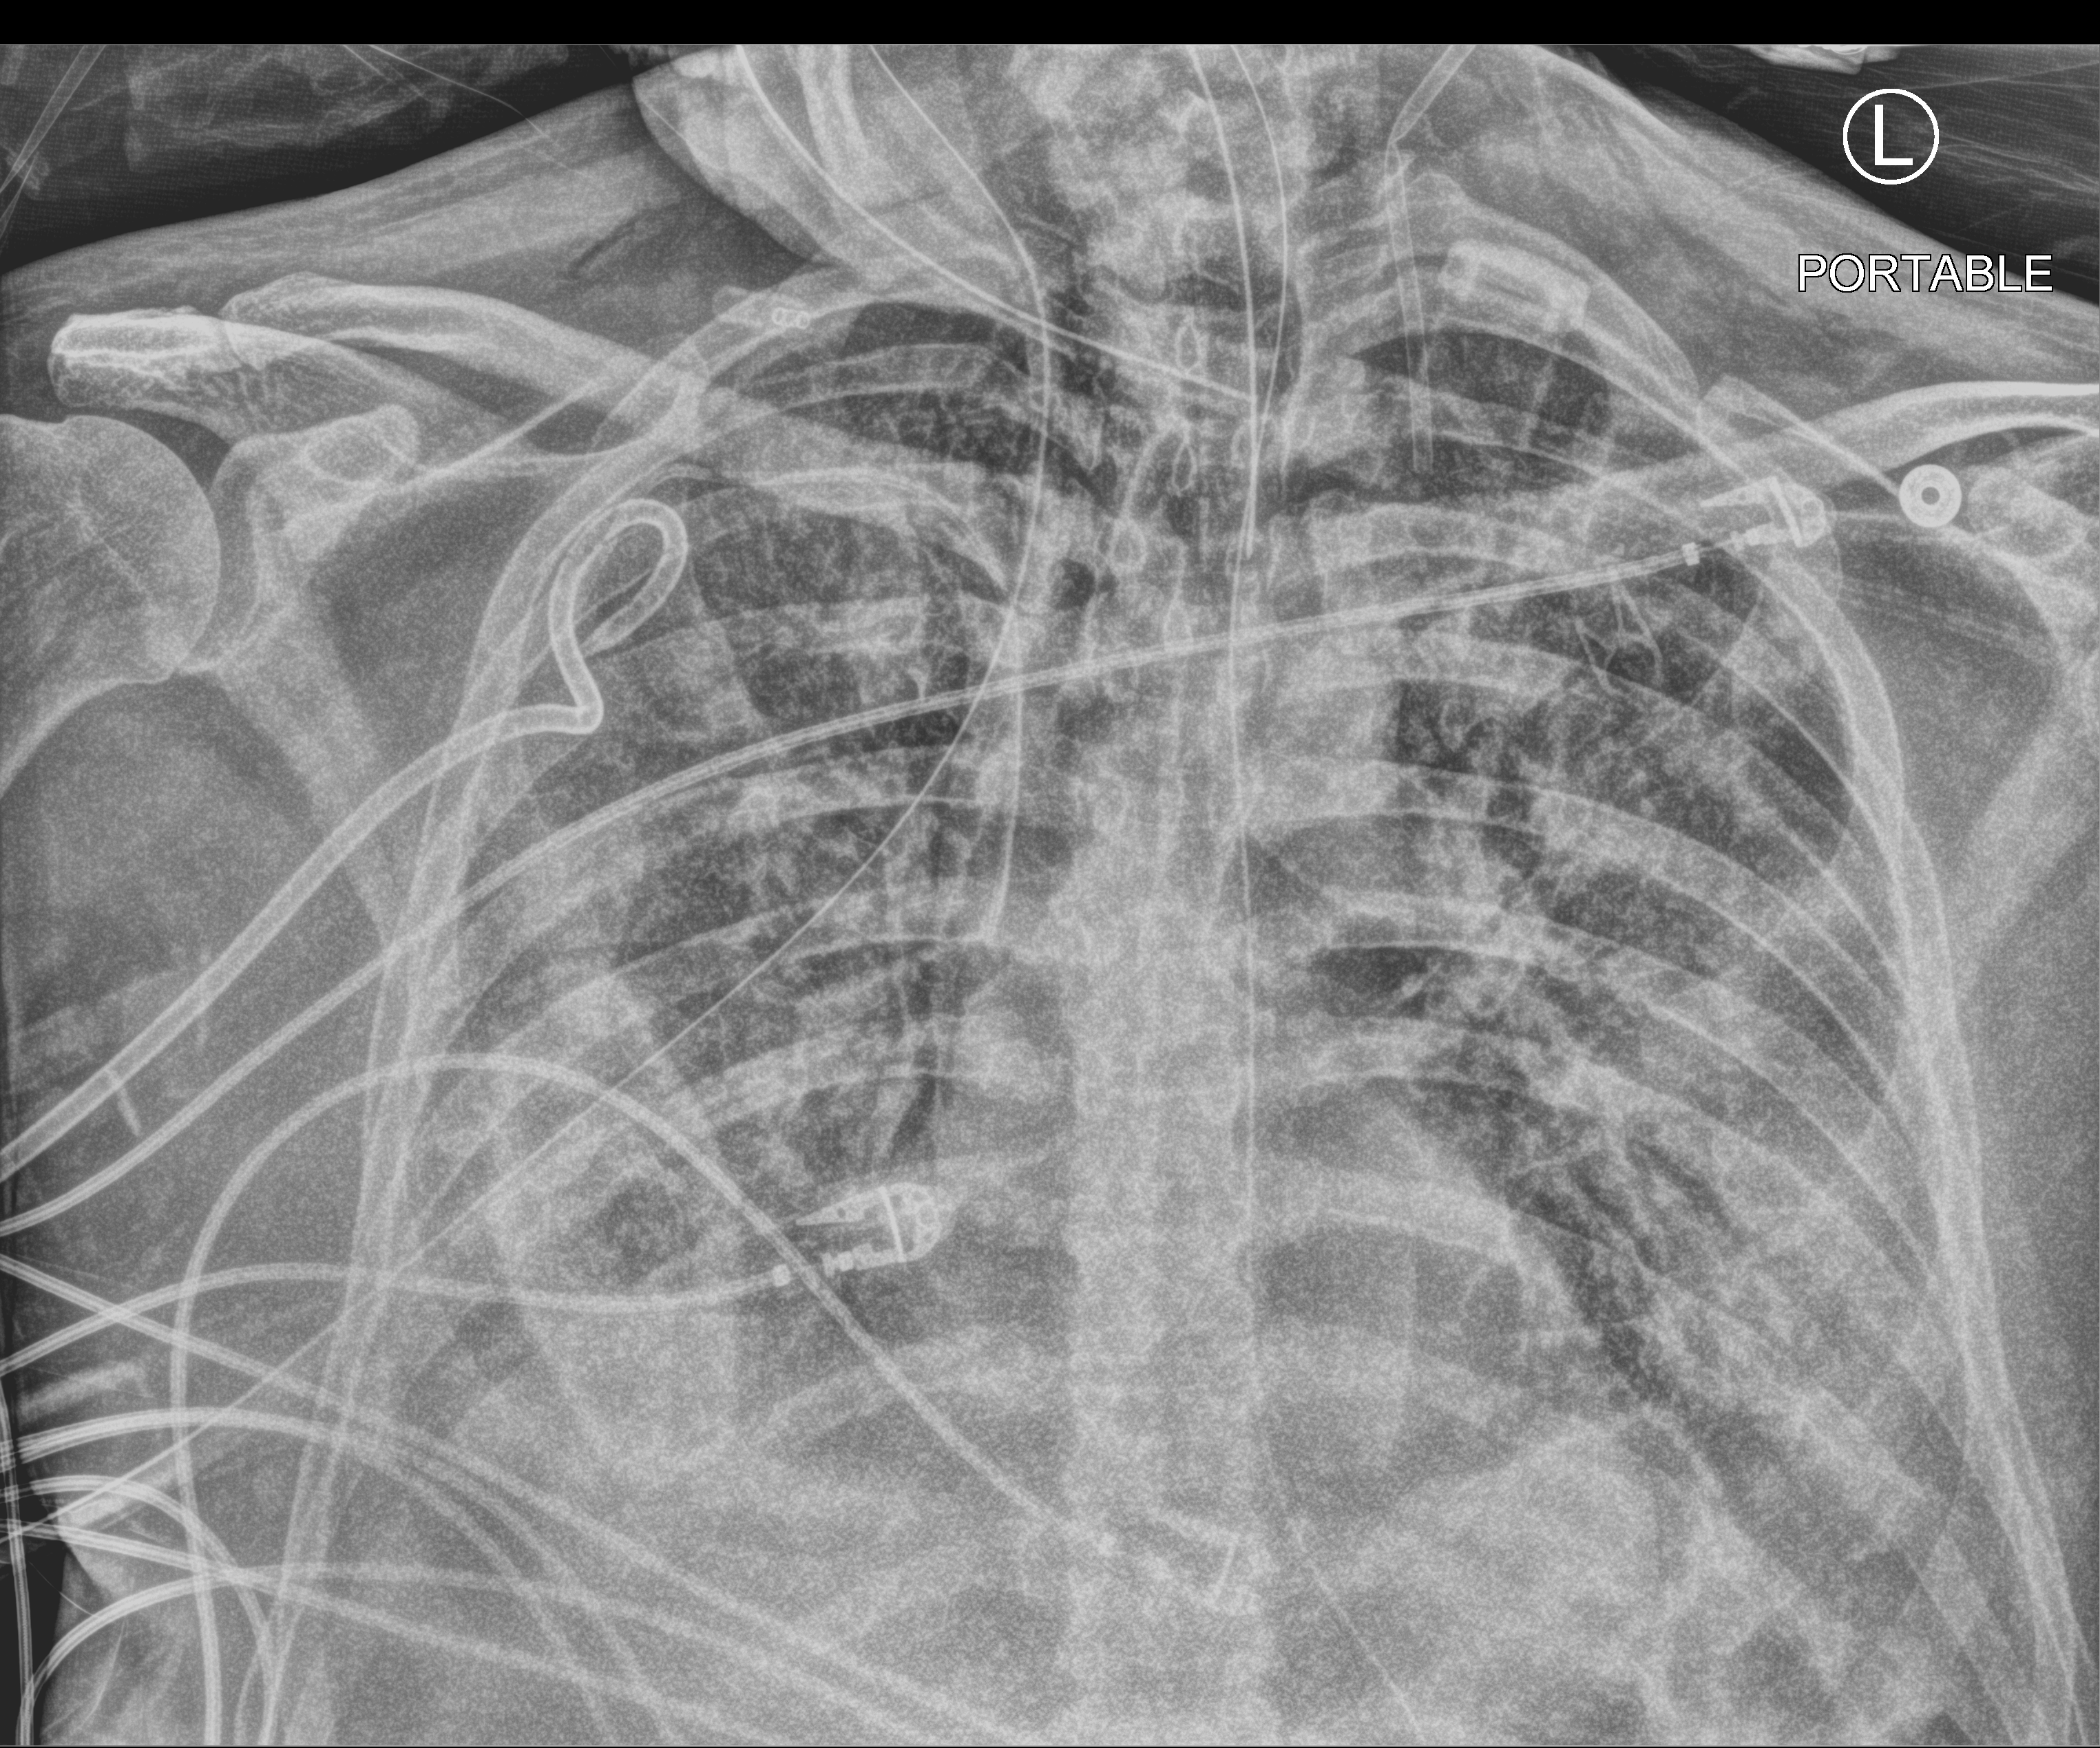
Chest X-ray (portable), anteroposterior (AP) projection. Male patient hospitalised with COVID-19, age 60–74 years.
Admission-level facts for this patient (not findings on this image; timing relative to this image not recorded):
- length of hospital stay: 8 days